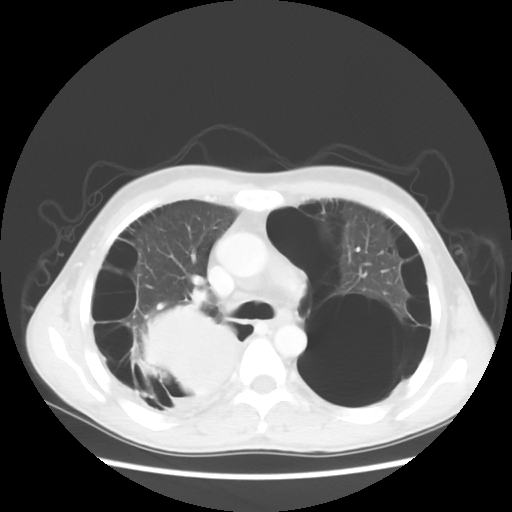
Chest CT, one axial slice. Slice 36 of 56 in the series (ordered by position). Reconstruction kernel STANDARD. 140 kVp. Lung window (W 1500 / L -600 HU). 5 mm slice thickness. 512 × 512 image matrix, field of view 351 × 351 mm. Patient: male, 41 years. Case-level facts recorded for this patient, not image findings: clinical TNM (as recorded): T4 N0 M1a; histopathological grade: G3.
Structures marked on this image (bounding box drawn by a radiologist):
- lung tumour (recorded histology: large cell carcinoma): box from (x=137, y=300) to (x=242, y=407) px